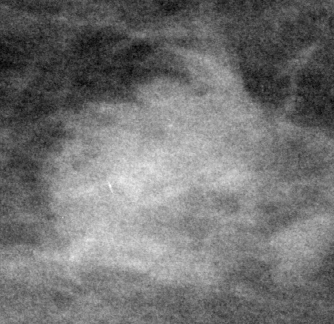
Cropped region of a digitized screen-film mammogram centred on a radiologist-marked abnormality, left breast, MLO view, BI-RADS breast density category 1 (scale 1–4).
Marked abnormality: mass, shape oval, margins microlobulated; BI-RADS assessment category 4; pathology (as recorded): malignant.